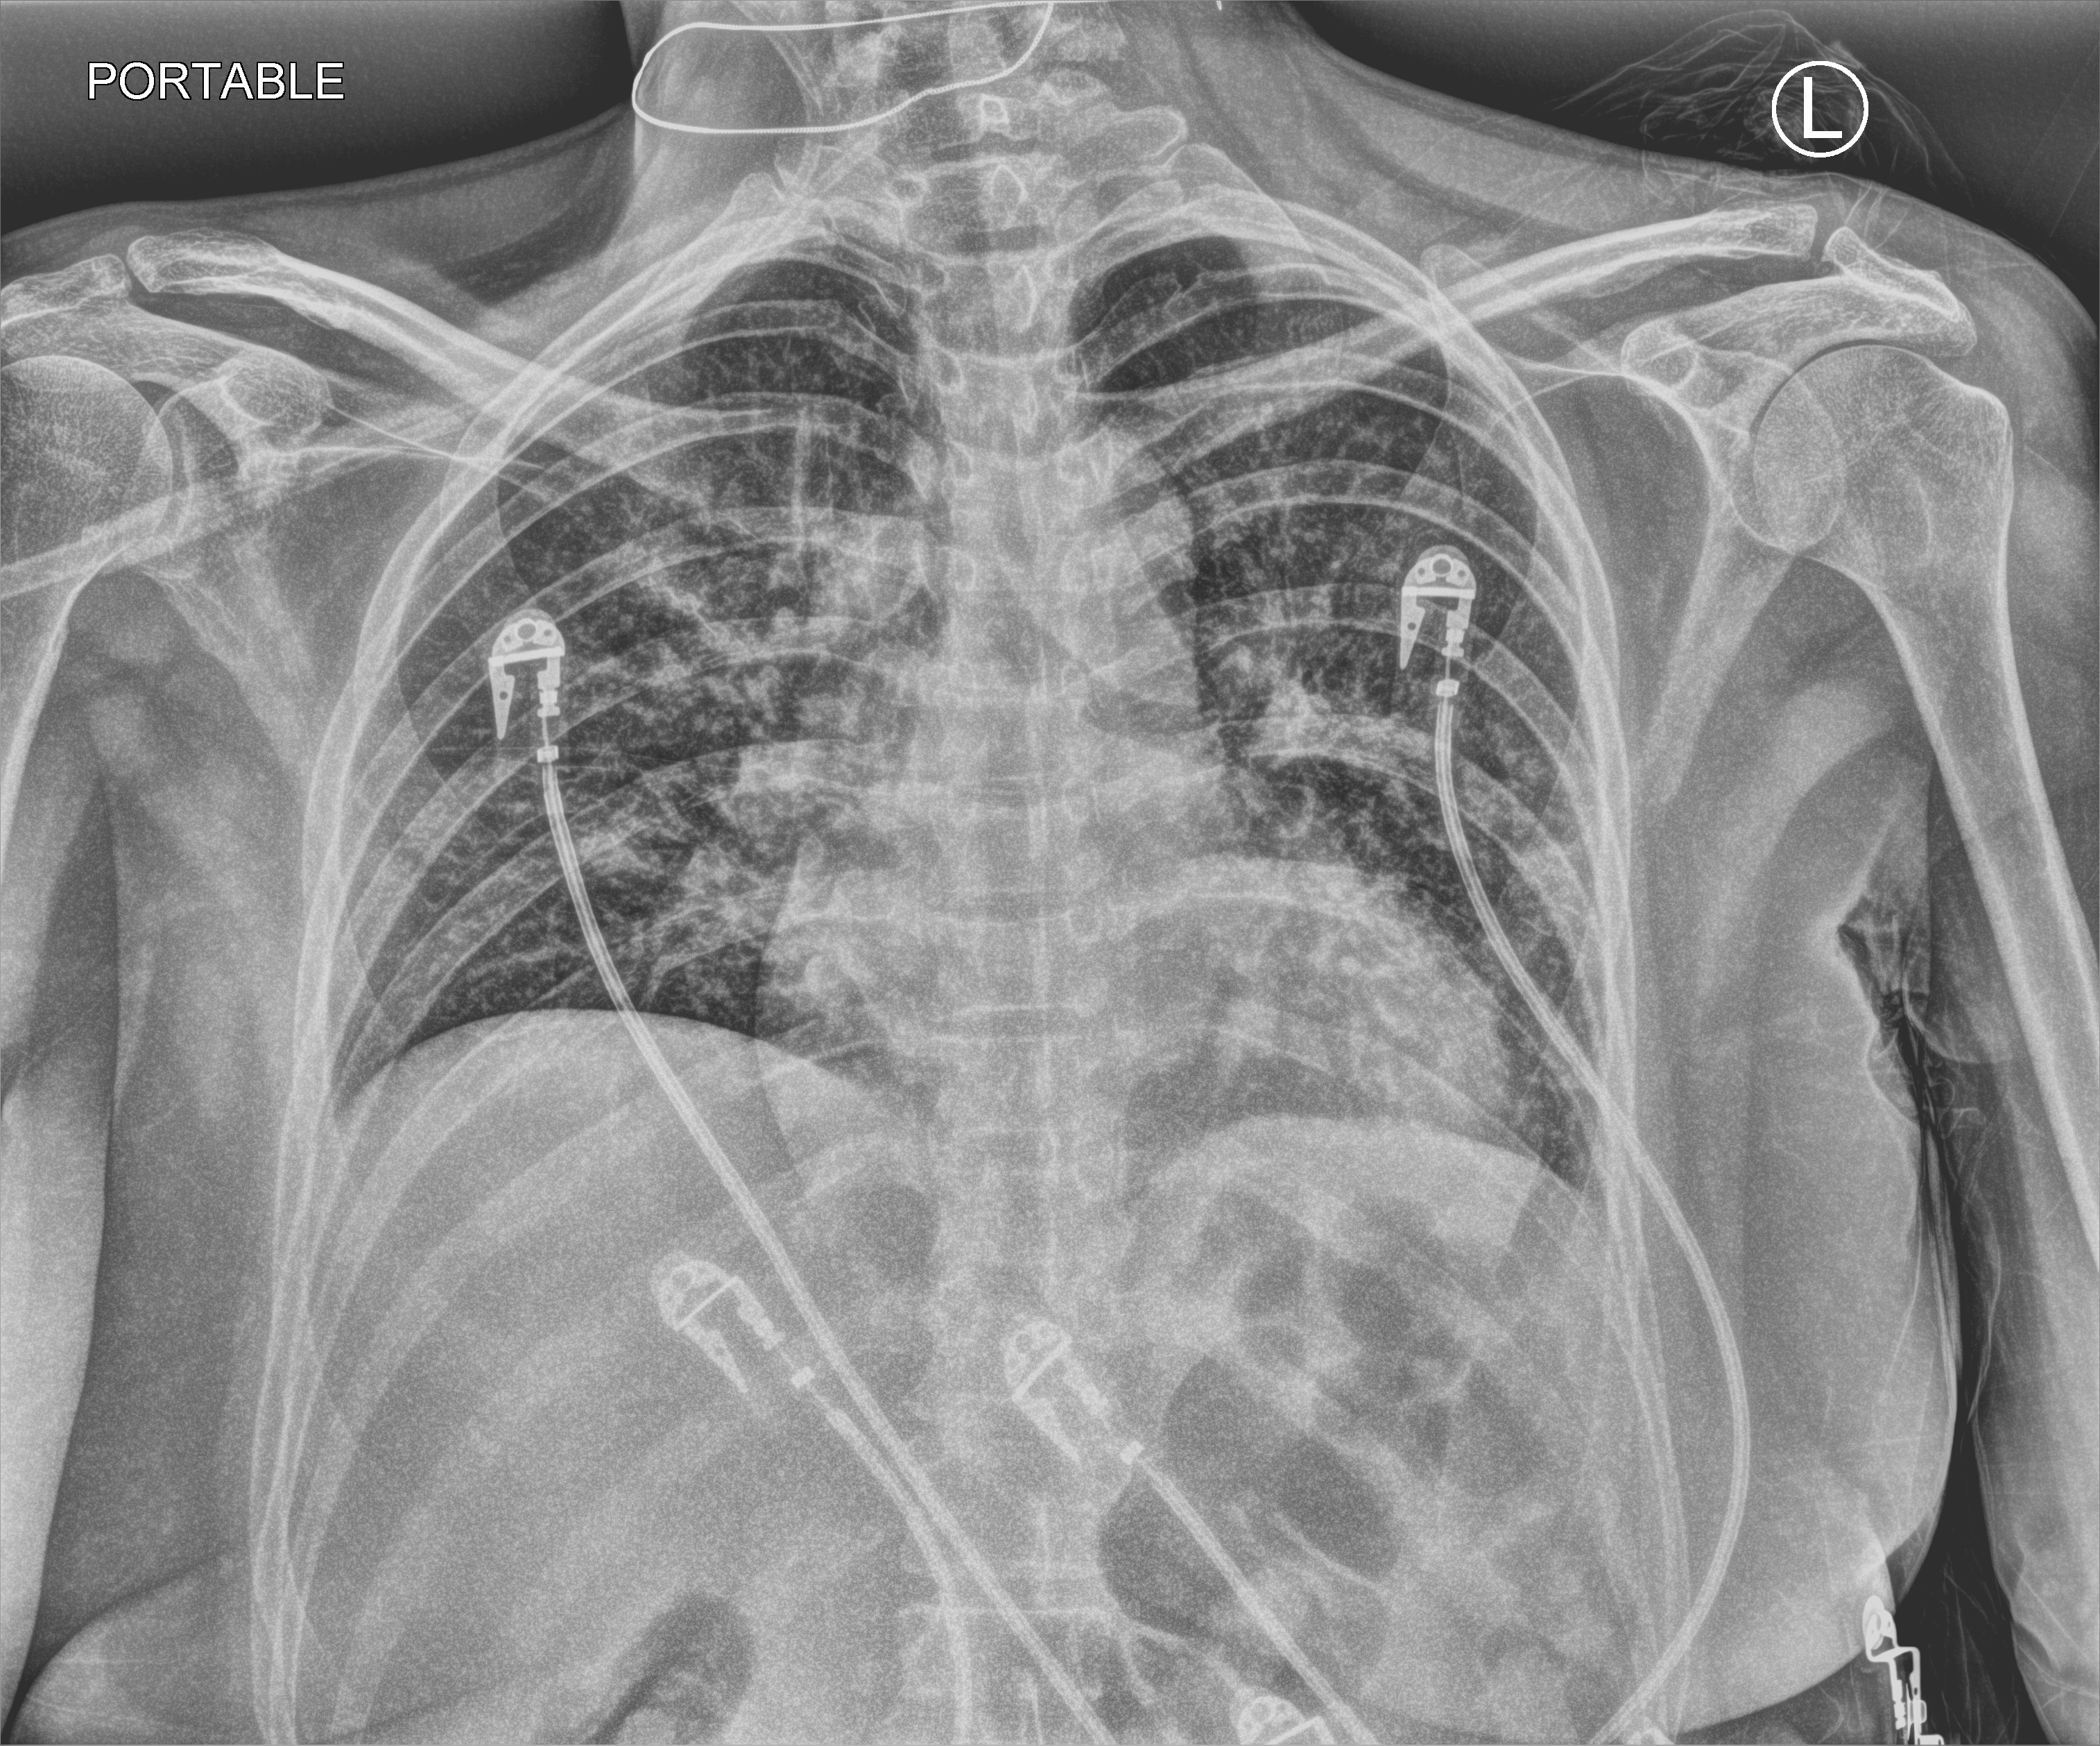
Bedside chest radiograph (computed radiography); anteroposterior (AP) projection. Female patient hospitalised with COVID-19, age 18–59 years.
From the hospital-stay record, not from the radiograph (when in the stay this image was taken is not recorded): mechanically ventilated during this hospital stay: no.